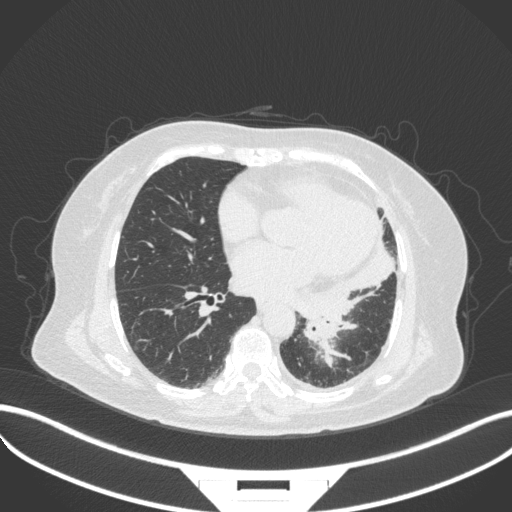
Chest CT, one axial slice; slice 151 of 328 in the series (ordered by position); 120 kVp; lung window (W 1500 / L -600 HU); 512 × 512 image matrix, field of view 400 × 400 mm. Female patient, age 69 years. From the clinical record (not read from this slice): clinical TNM (as recorded): T2b N3 M1.
Annotated regions visible in this slice (bounding box drawn by a radiologist):
- lung tumour (recorded histology: adenocarcinoma): bounding box (x1, y1, x2, y2) in pixels: (302, 314, 362, 371)